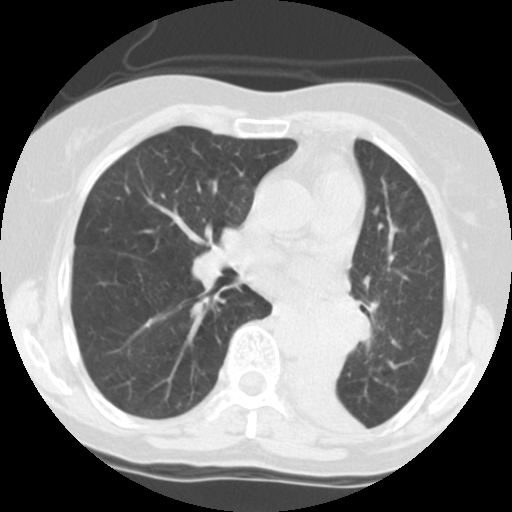
Low-dose screening chest CT, one axial slice; position 68 of 113 along the scan axis; reconstruction kernel STANDARD; 140 kVp; lung window (W 1500 / L -600 HU); 2.5 mm slice thickness; 512 × 512 image matrix, field of view 280 × 280 mm.
Structures marked on this image (outlined manually by an expert reader):
- lesion 1 (tumor, left main bronchus): box from (x=299, y=296) to (x=368, y=361) px